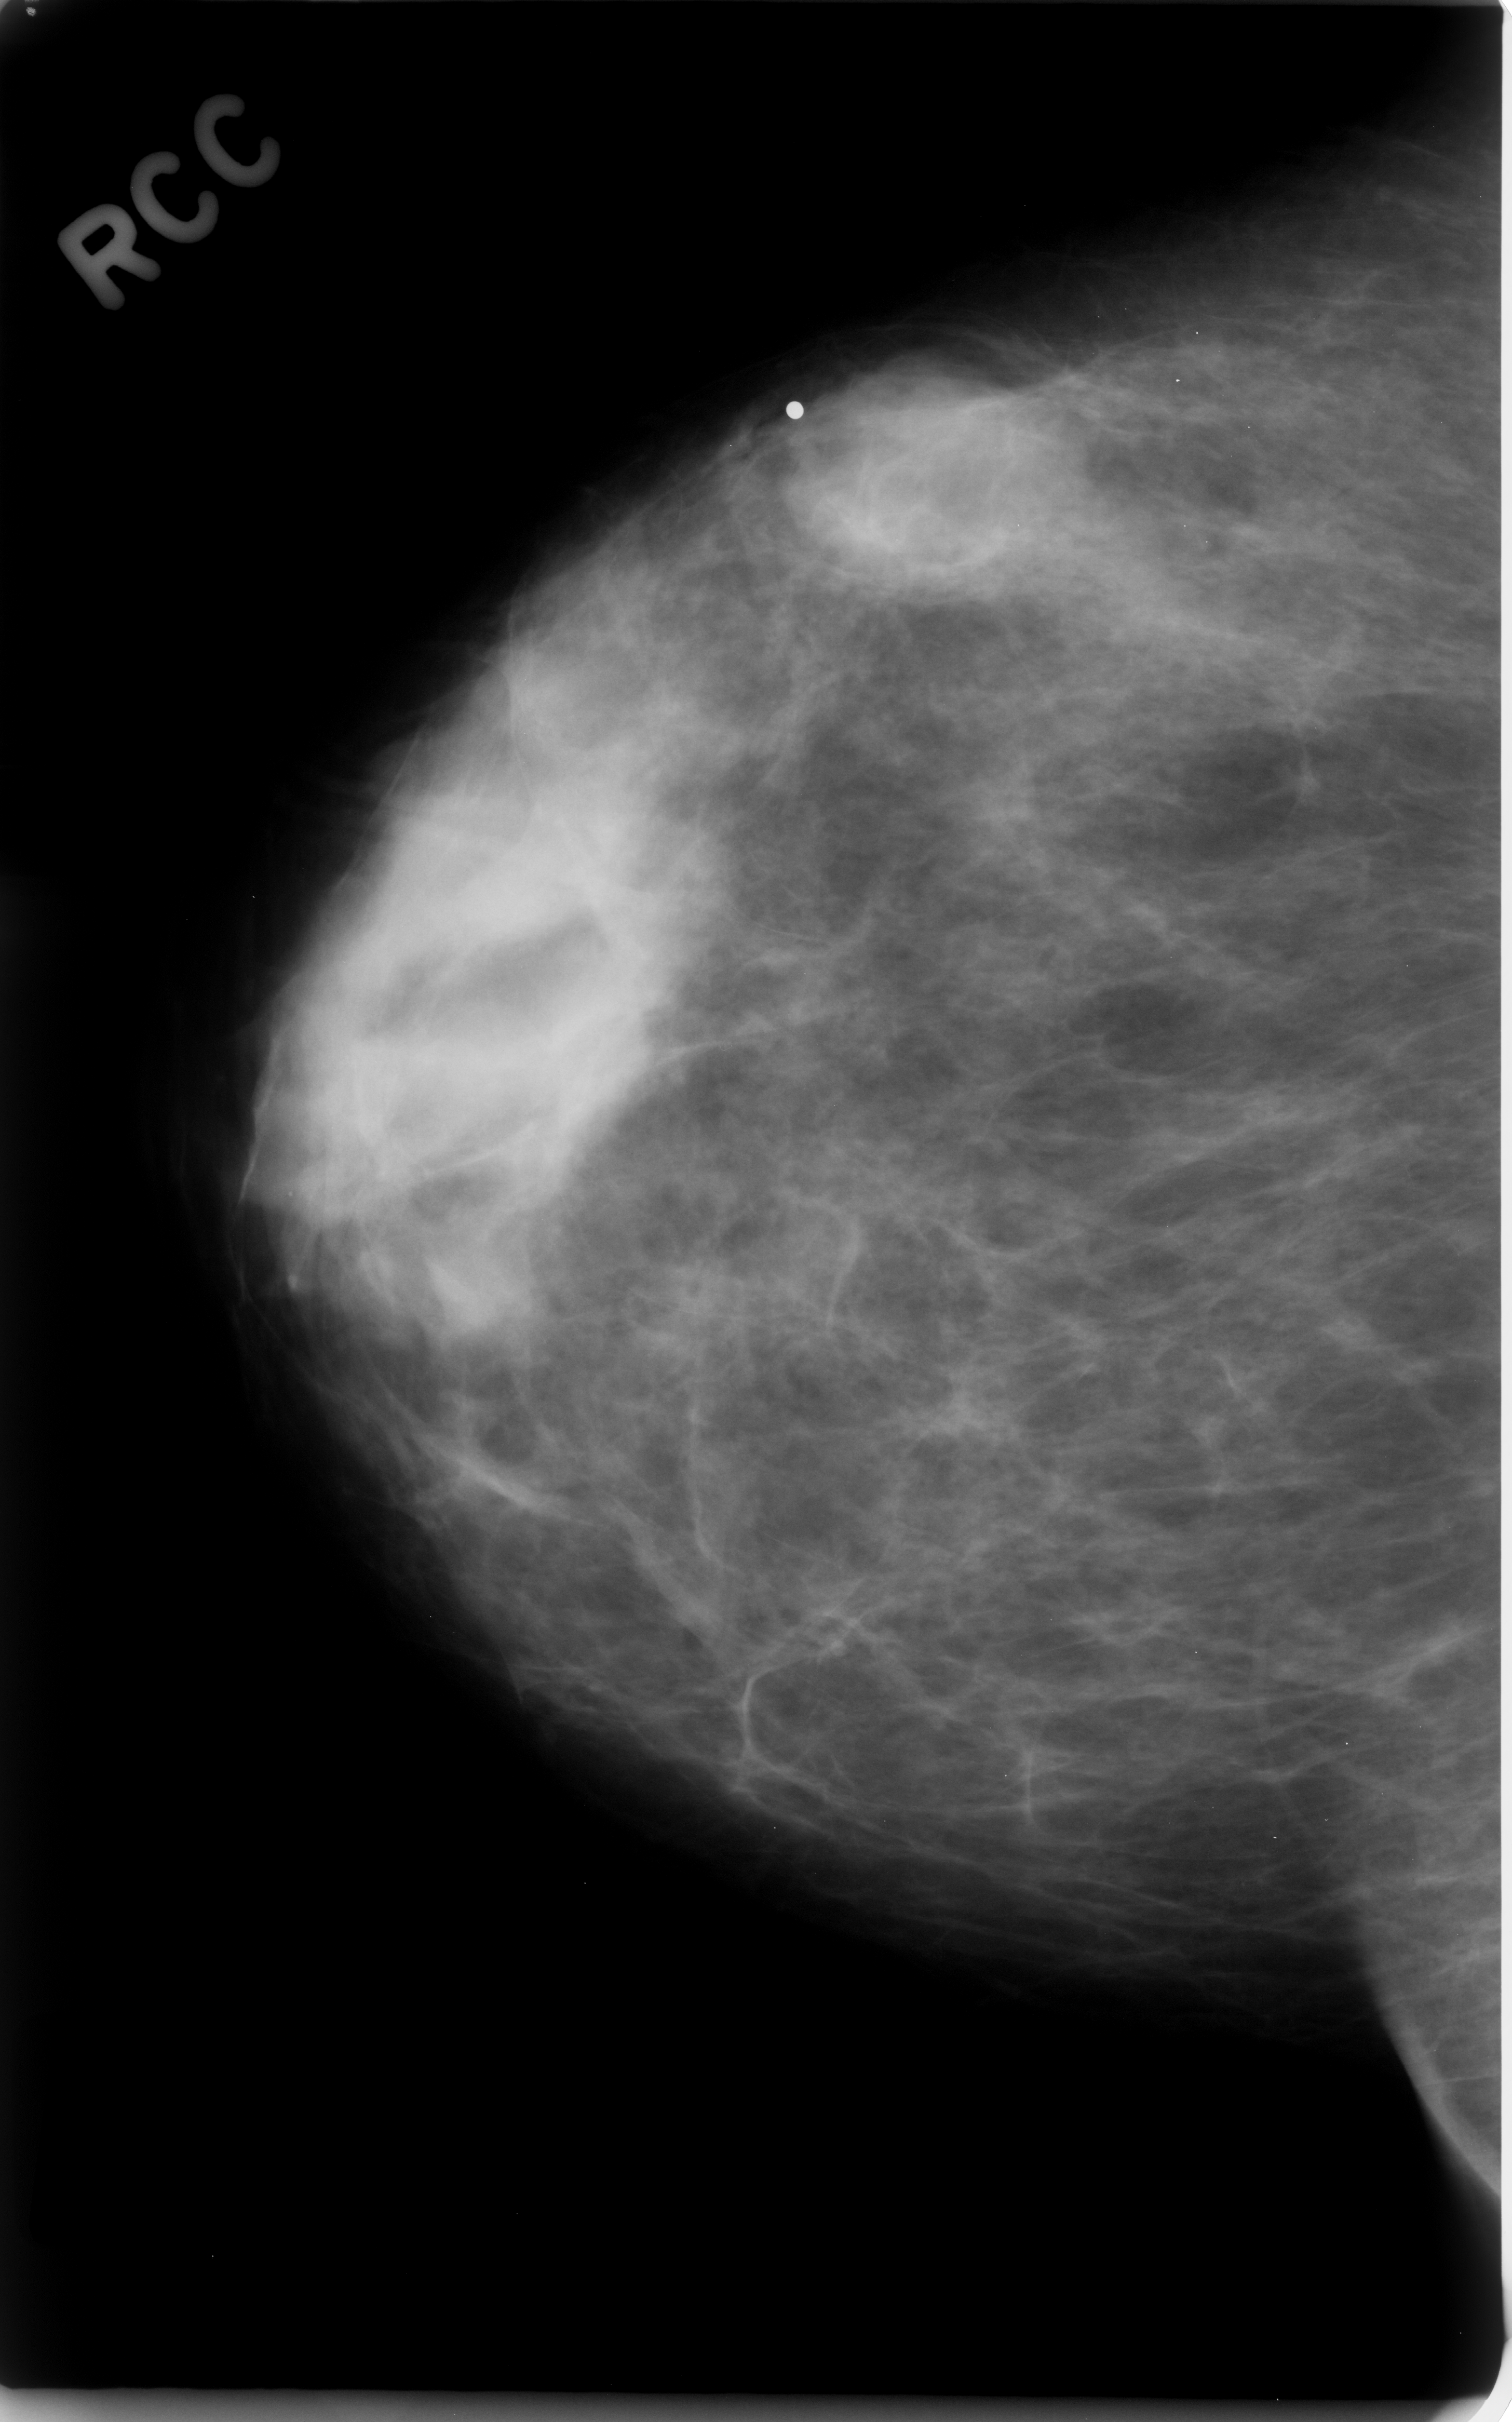
Digitized screen-film mammogram. Right breast. CC view. Breast composition: scattered fibroglandular densities (BI-RADS density category 2 of 4). 1512 × 2422 image matrix.
Expert-marked regions of interest on this image (one box per marked abnormality):
- mass, shape lobulated, margins obscured; BI-RADS assessment category 4; pathology result (as recorded, not read from the image): benign: bounding box <784,340,1034,598> (left, top, right, bottom; pixels)